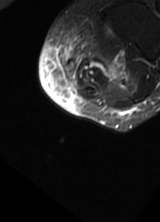
MRI of an extremity soft-tissue mass, one axial slice; slice 1 of 69 in the series (ordered by position); T2-weighted fat-saturated; MR volume resampled by the dataset authors to the PET/CT grid (not the native acquisition matrix); 3.27 mm slice thickness; 160 × 222 image matrix, field of view 156 × 217 mm. Female patient. Case-level facts recorded for this patient, not image findings: histological type: pleomorphic leiomyosarcoma; grade: high; site of the primary tumour: left thigh.
Outlined on this slice (expert contour drawn on MRI and transferred to this co-registered scan by the dataset authors):
- gross tumour volume including surrounding oedema: box from (x=61, y=27) to (x=128, y=94) px